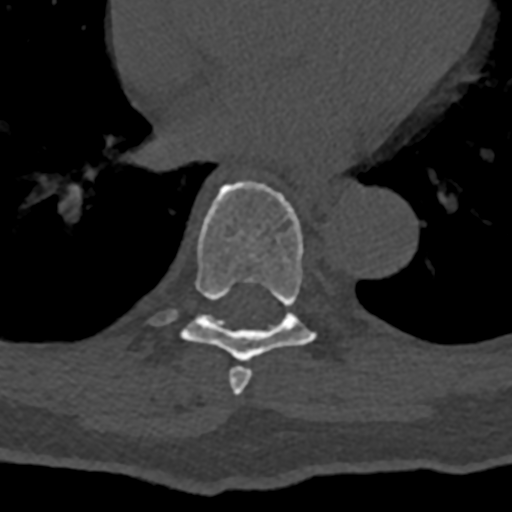
CT including the spine, one axial slice. Slice 709 of 797 in the series (ordered by position). Reconstruction kernel Br40s/3. 120 kVp. Bone window (W 1800 / L 400 HU). 0.5 mm slice thickness. 512 × 512 image matrix, field of view 160 × 160 mm. Male patient, age 74 years. From the clinical record (not read from this slice): primary cancer: renal; vertebrae with lytic lesions (as recorded): T10, L1, L2, L3, L4, L5.
Outlined on this slice (semi-automatically segmented with operator editing):
- T7 vertebra: bounding box <229,366,252,396> (left, top, right, bottom; pixels)
- T8 vertebra: <149,181,332,361>